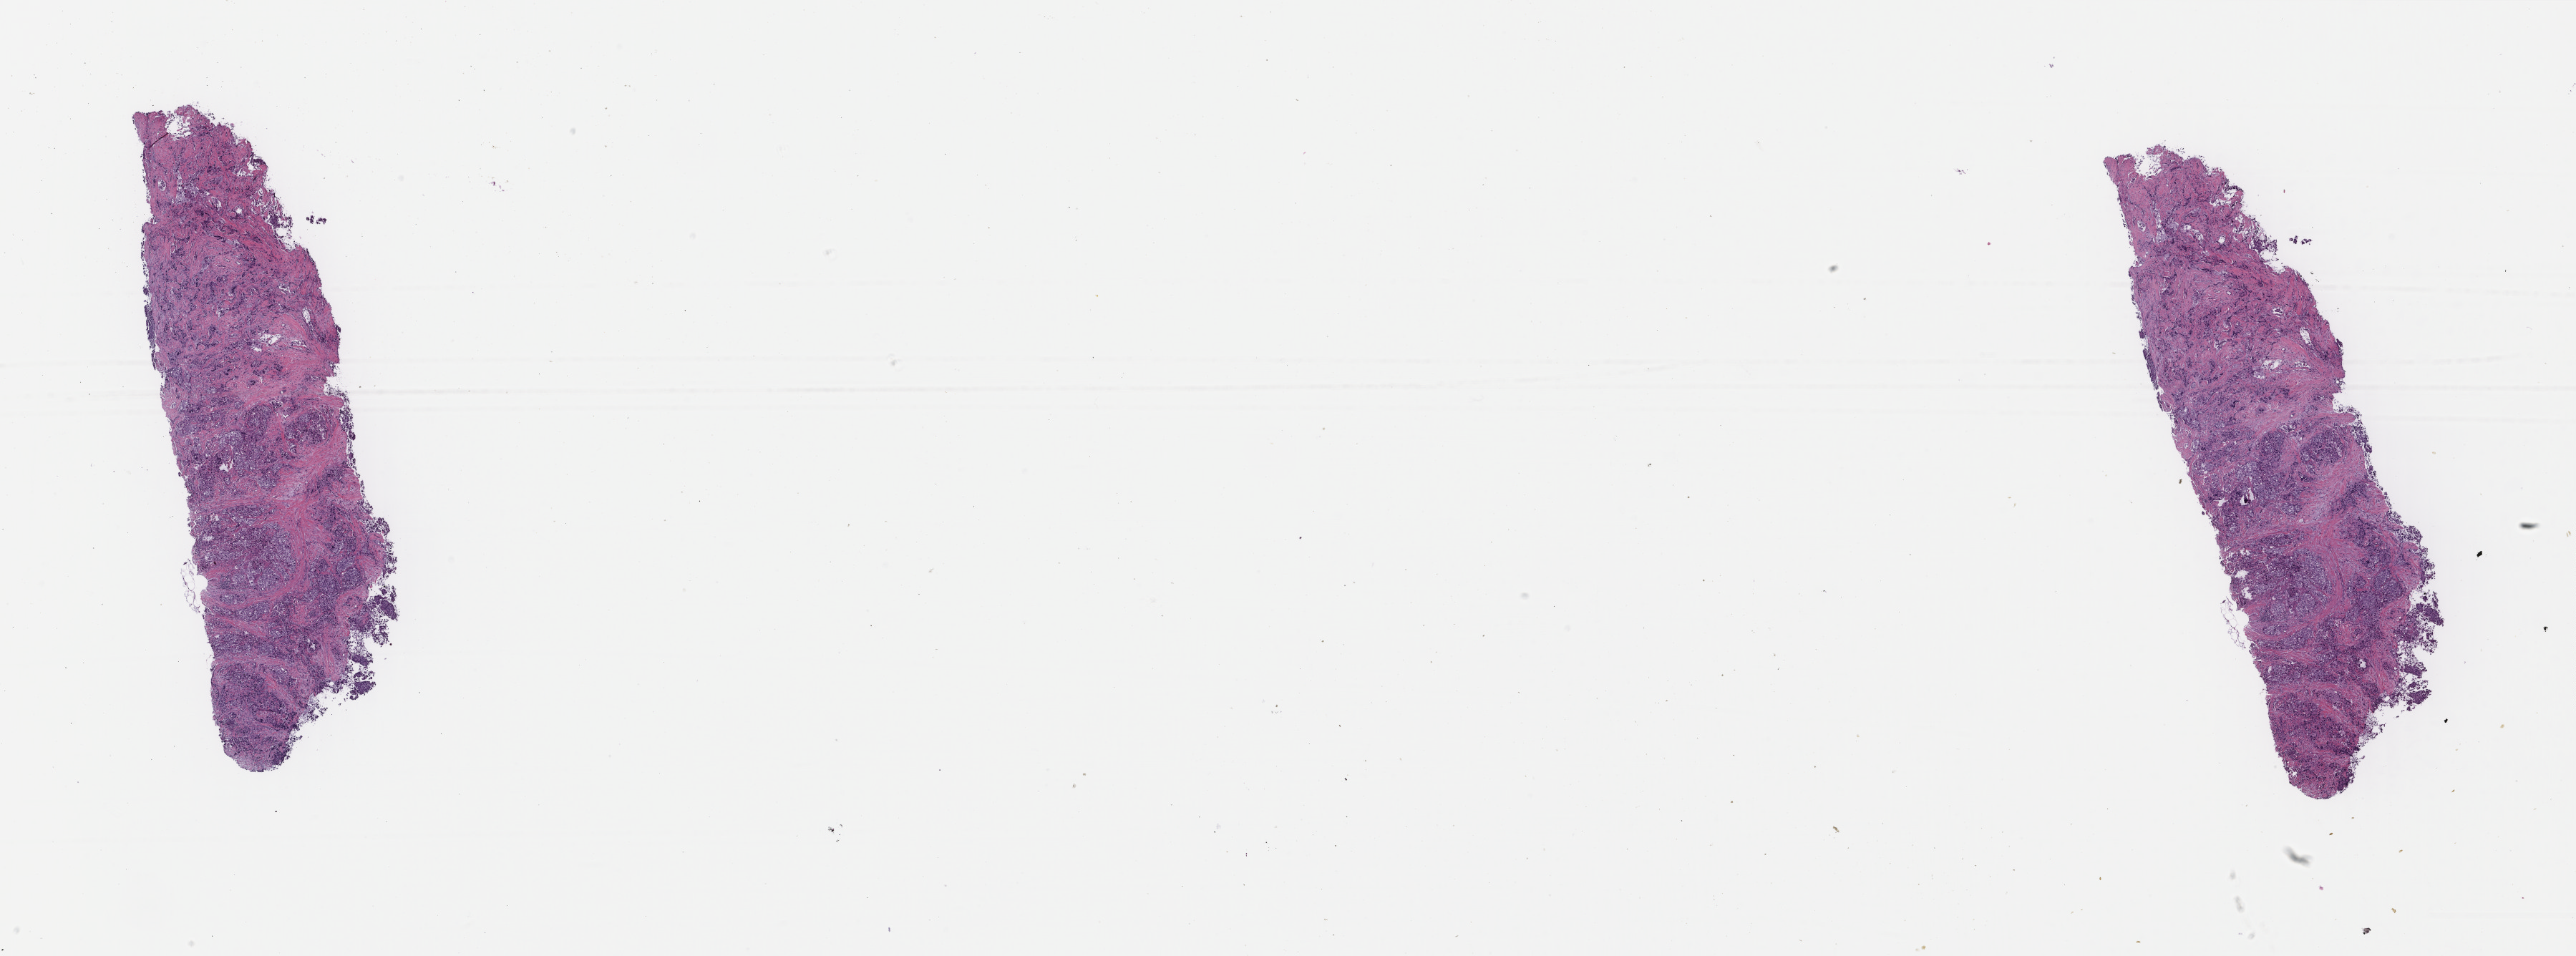
Digitized Hematoxylin and eosin (H&E) stained tissue section (whole slide) — shown as a low-resolution overview of the whole scanned area (about 28.6 x 10.6 mm, acquisition: 40x scan); FFPE section; breast, primary tumour sample. Patient: female, age at initial diagnosis 65 years.
* pathologic diagnosis: Infiltrating duct carcinoma, NOS
* AJCC pathologic stage: IIA (7th edition)
* laterality: left
* TNM: T2 N0 M0